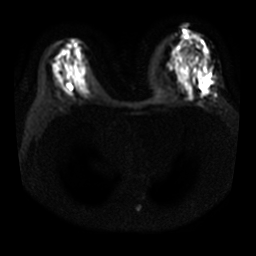
Breast MRI, one axial slice; slice 16 of 29 in the series (ordered by position); diffusion-weighted series; image 2 of 4 stored at this slice position (different b-values; order by instance number); 3 T; 256 × 256 image matrix, field of view 340 × 340 mm. Female patient.
Outlined on this slice (expert manual segmentation):
- tumour on diffusion-weighted imaging: bounding box [x1, y1, x2, y2] px = [201, 65, 210, 84]